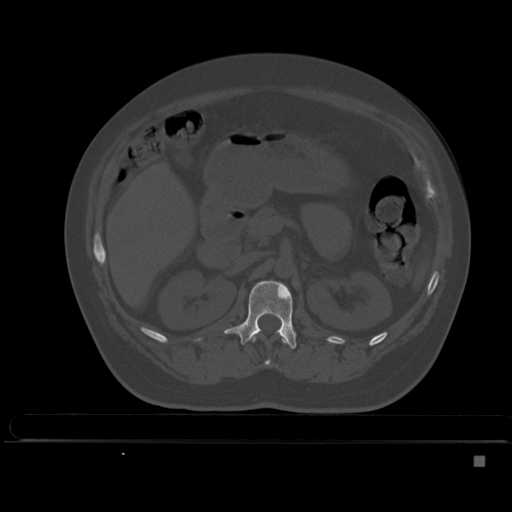
CT including the spine, one axial slice; position 199 of 495 along the scan axis; bone window (W 1800 / L 400 HU); 1.5 mm slice thickness; 512 × 512 image matrix, field of view 404 × 404 mm. Female patient, age 33 years. Case-level facts recorded for this patient, not image findings: primary cancer: breast; vertebrae with lytic lesions (as recorded): T1.
Outlined on this slice (semi-automatically segmented with operator editing):
- L1 vertebra: bounding box [x1, y1, x2, y2] px = [224, 280, 297, 349]
- T12 vertebra: [251, 335, 288, 366]